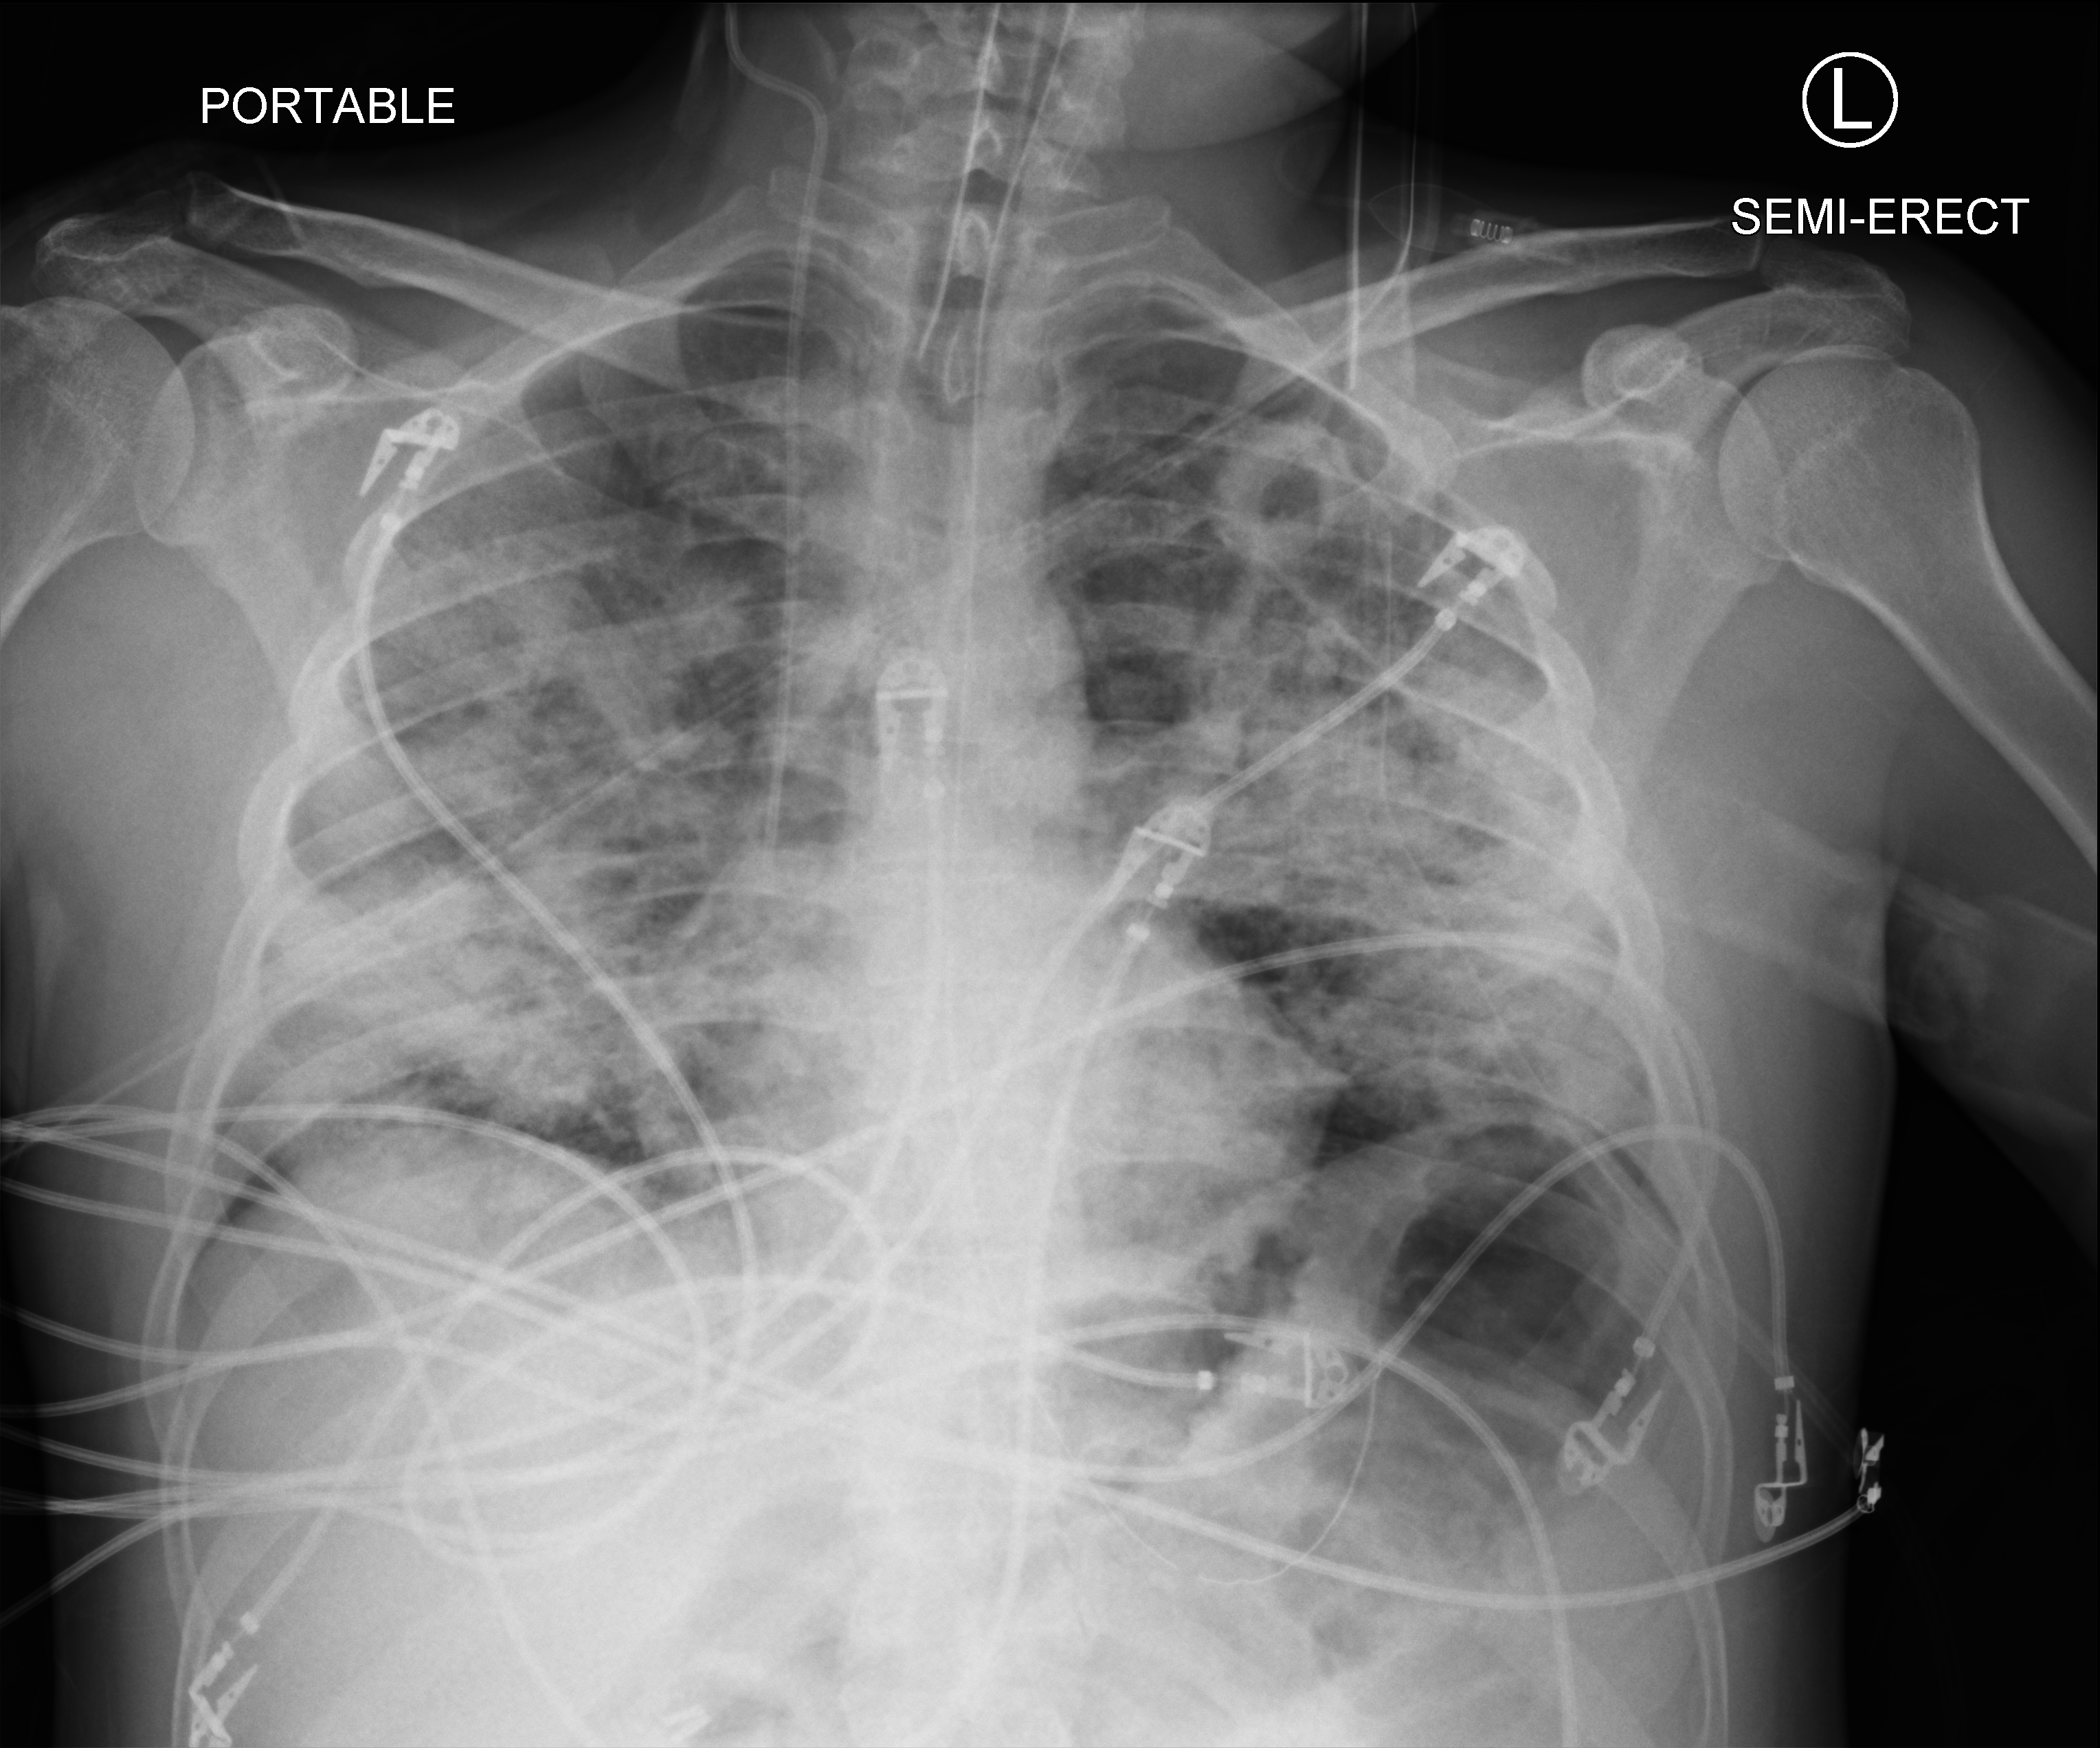
Portable chest radiograph; anteroposterior (AP) projection. Patient hospitalised with COVID-19; male, aged 18–59 years.
Admission-level facts for this patient (not findings on this image; timing relative to this image not recorded):
- admitted to intensive care during this hospital stay: yes
- mechanically ventilated during this hospital stay: yes